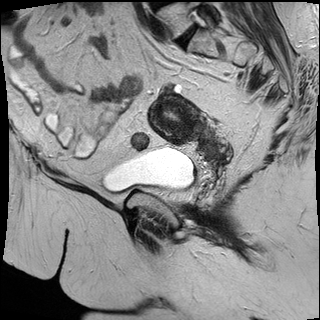
Pelvic MRI for cervical cancer, one sagittal slice. Slice 14 of 32 in the series (ordered by position). T2-weighted. 1.5 T. TE 87 ms, TR 3063.4 ms. 4 mm slice thickness. 320 × 320 image matrix, field of view 280 × 280 mm. Patient: female, 53 years.
Outlined on this slice (outlined manually by an expert reader):
- uterus and cervix: bounding box <148,93,219,162> (left, top, right, bottom; pixels)